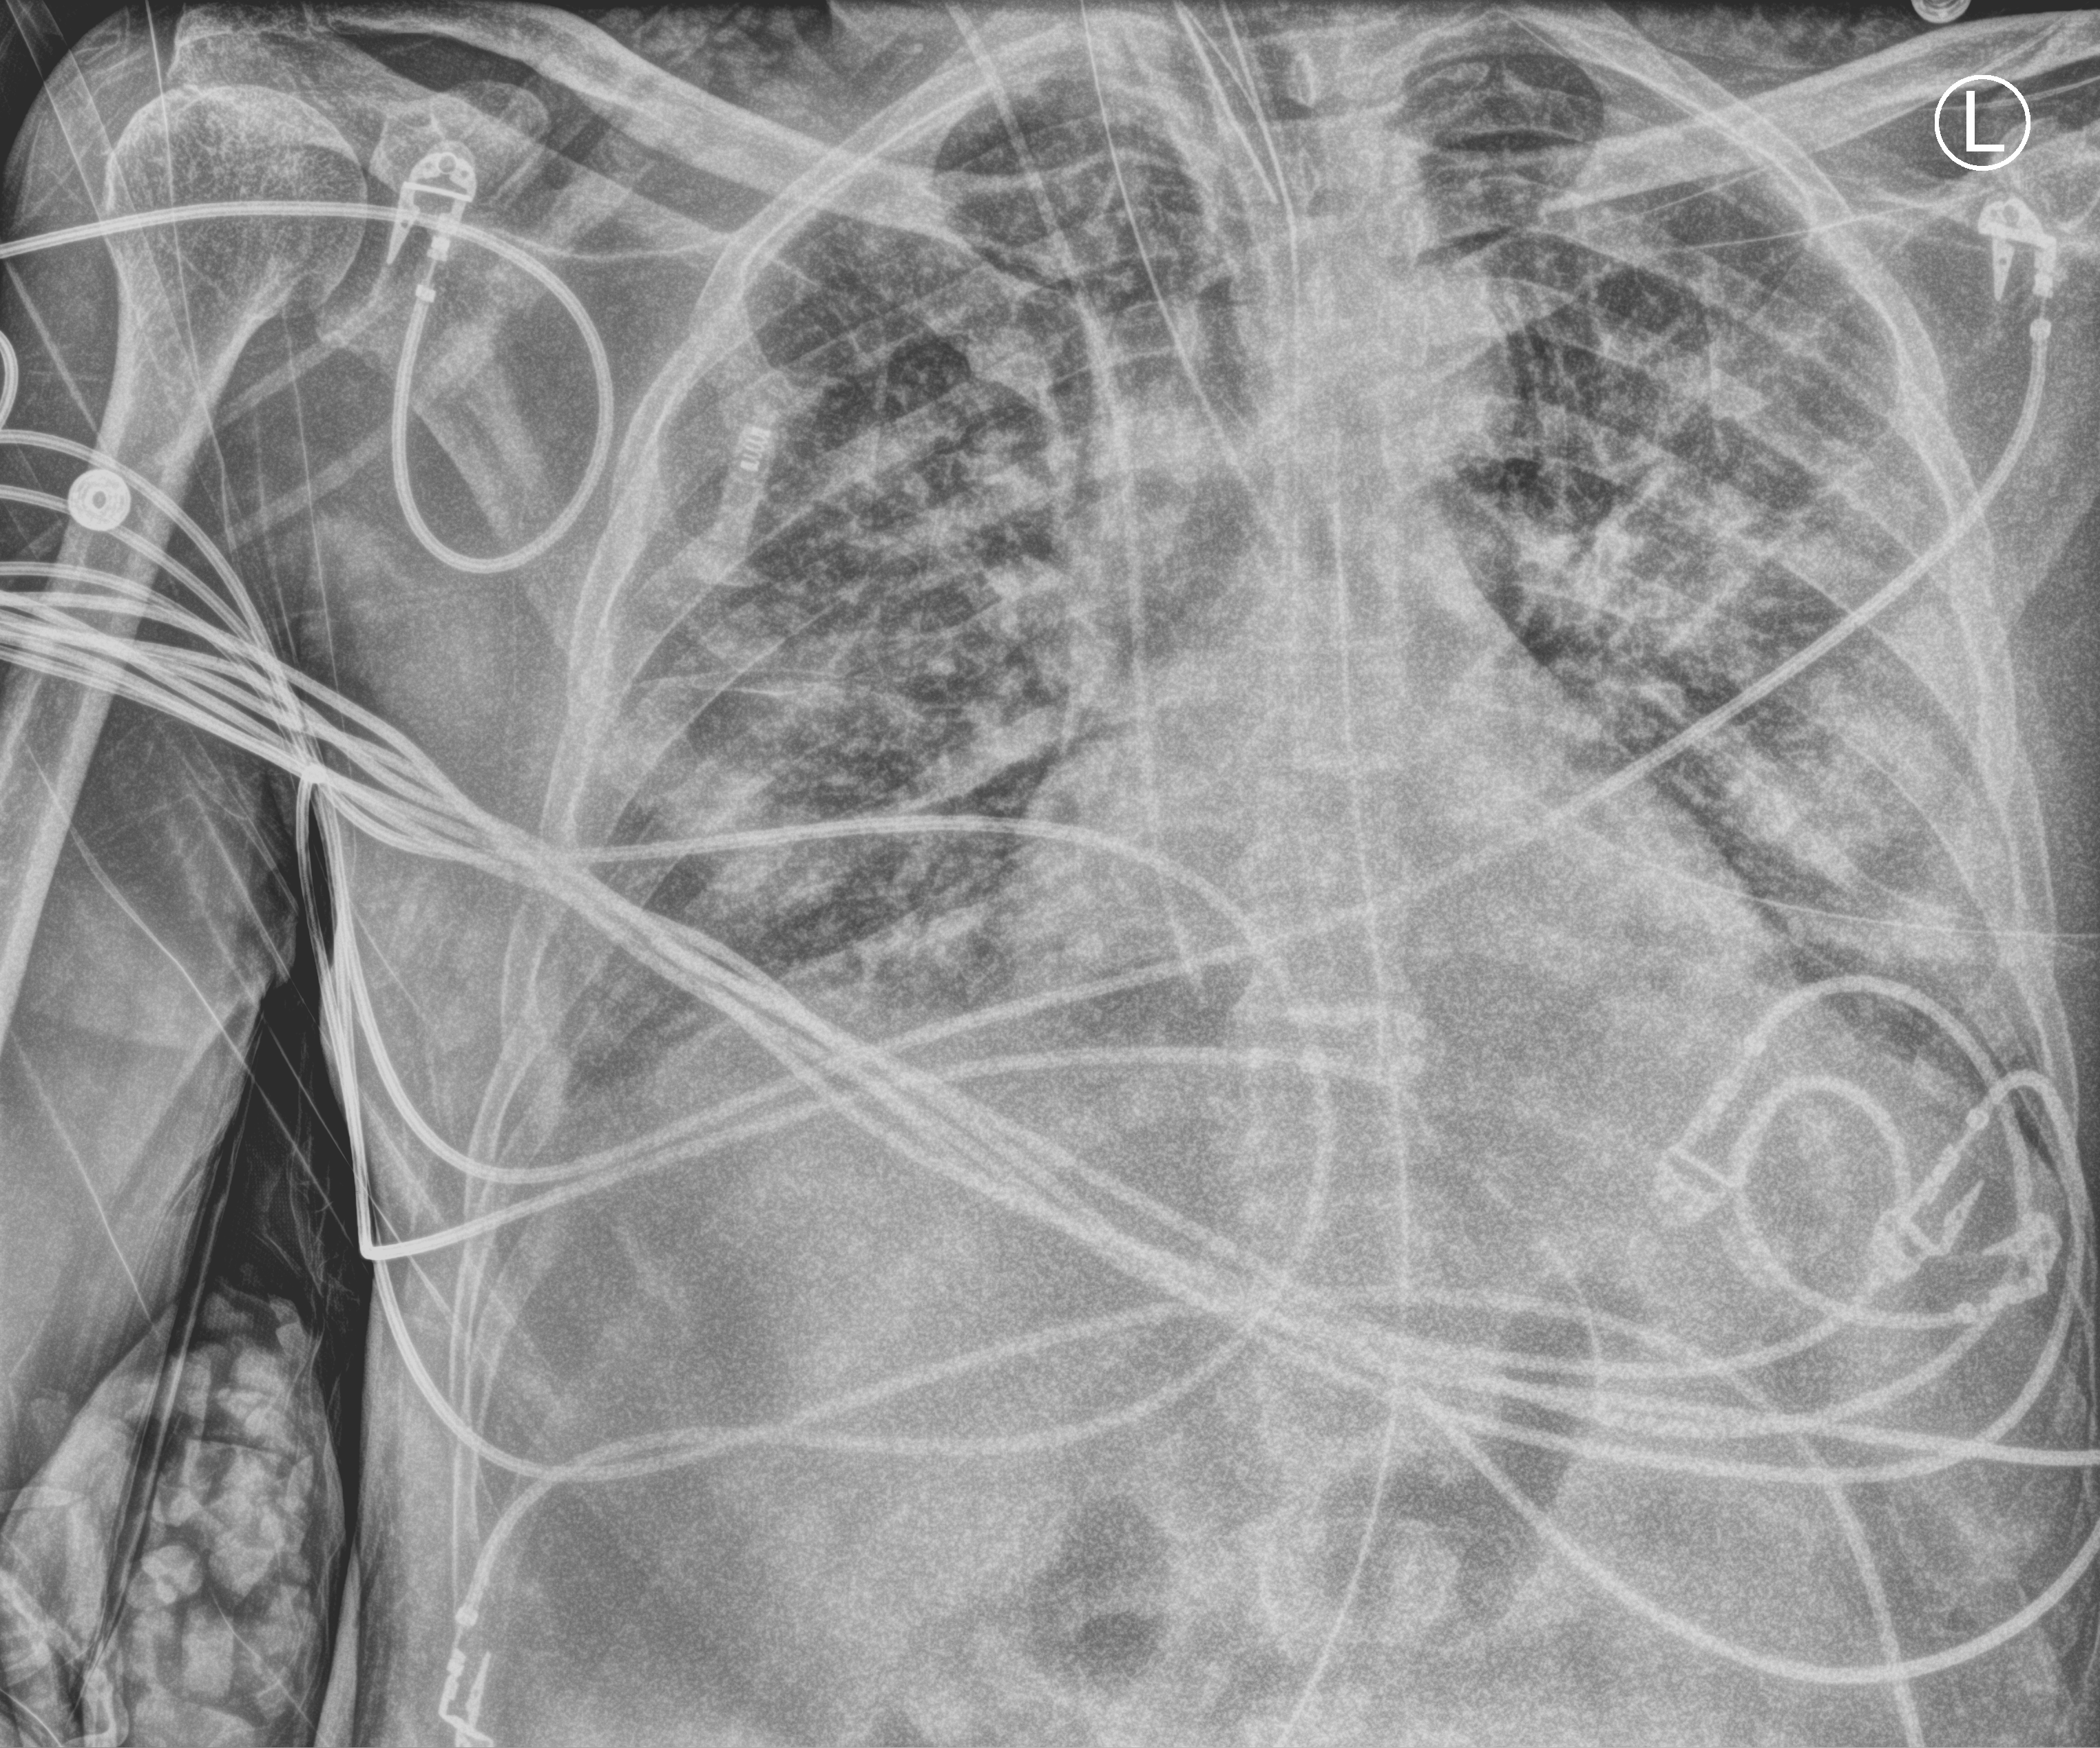
Chest X-ray (portable), anteroposterior (AP) projection. Patient hospitalised with COVID-19; male, aged 18–59 years.
Hospital-stay facts (about this admission, not read from this image; timing relative to this image not recorded): length of hospital stay: 41 days; mechanically ventilated during this hospital stay: yes; chronic kidney disease (admission record): no.